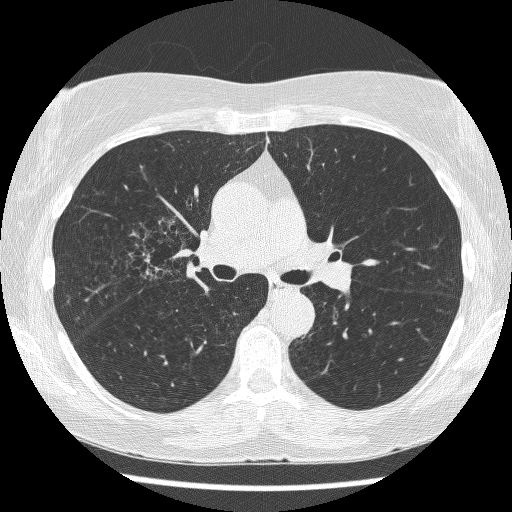
Low-dose screening chest CT, axial slice, first (baseline) screen, lung window (W 1500 / L -600 HU), lung (sharp) reconstruction kernel (BONE), slice 168 of 271 in the series. Female participant, aged 64 years at enrolment.
Lesion marked by an expert reader, bounding box <123,217,200,281> (left, top, right, bottom; pixels). The screening reader recorded 3 non-calcified nodules or masses ≥4 mm on this exam; which of them this box marks is not recorded. Official screen result: positive, change unspecified: nodule(s) >= 4 mm or enlarging nodule(s), mass(es), or other non-specific abnormalities suspicious for lung cancer. Lung cancer was diagnosed 735 days after this screen: adenocarcinoma, NOS, right upper lobe, right middle lobe, right hilum, stage IV (AJCC 6th edition), 85 mm at pathology.